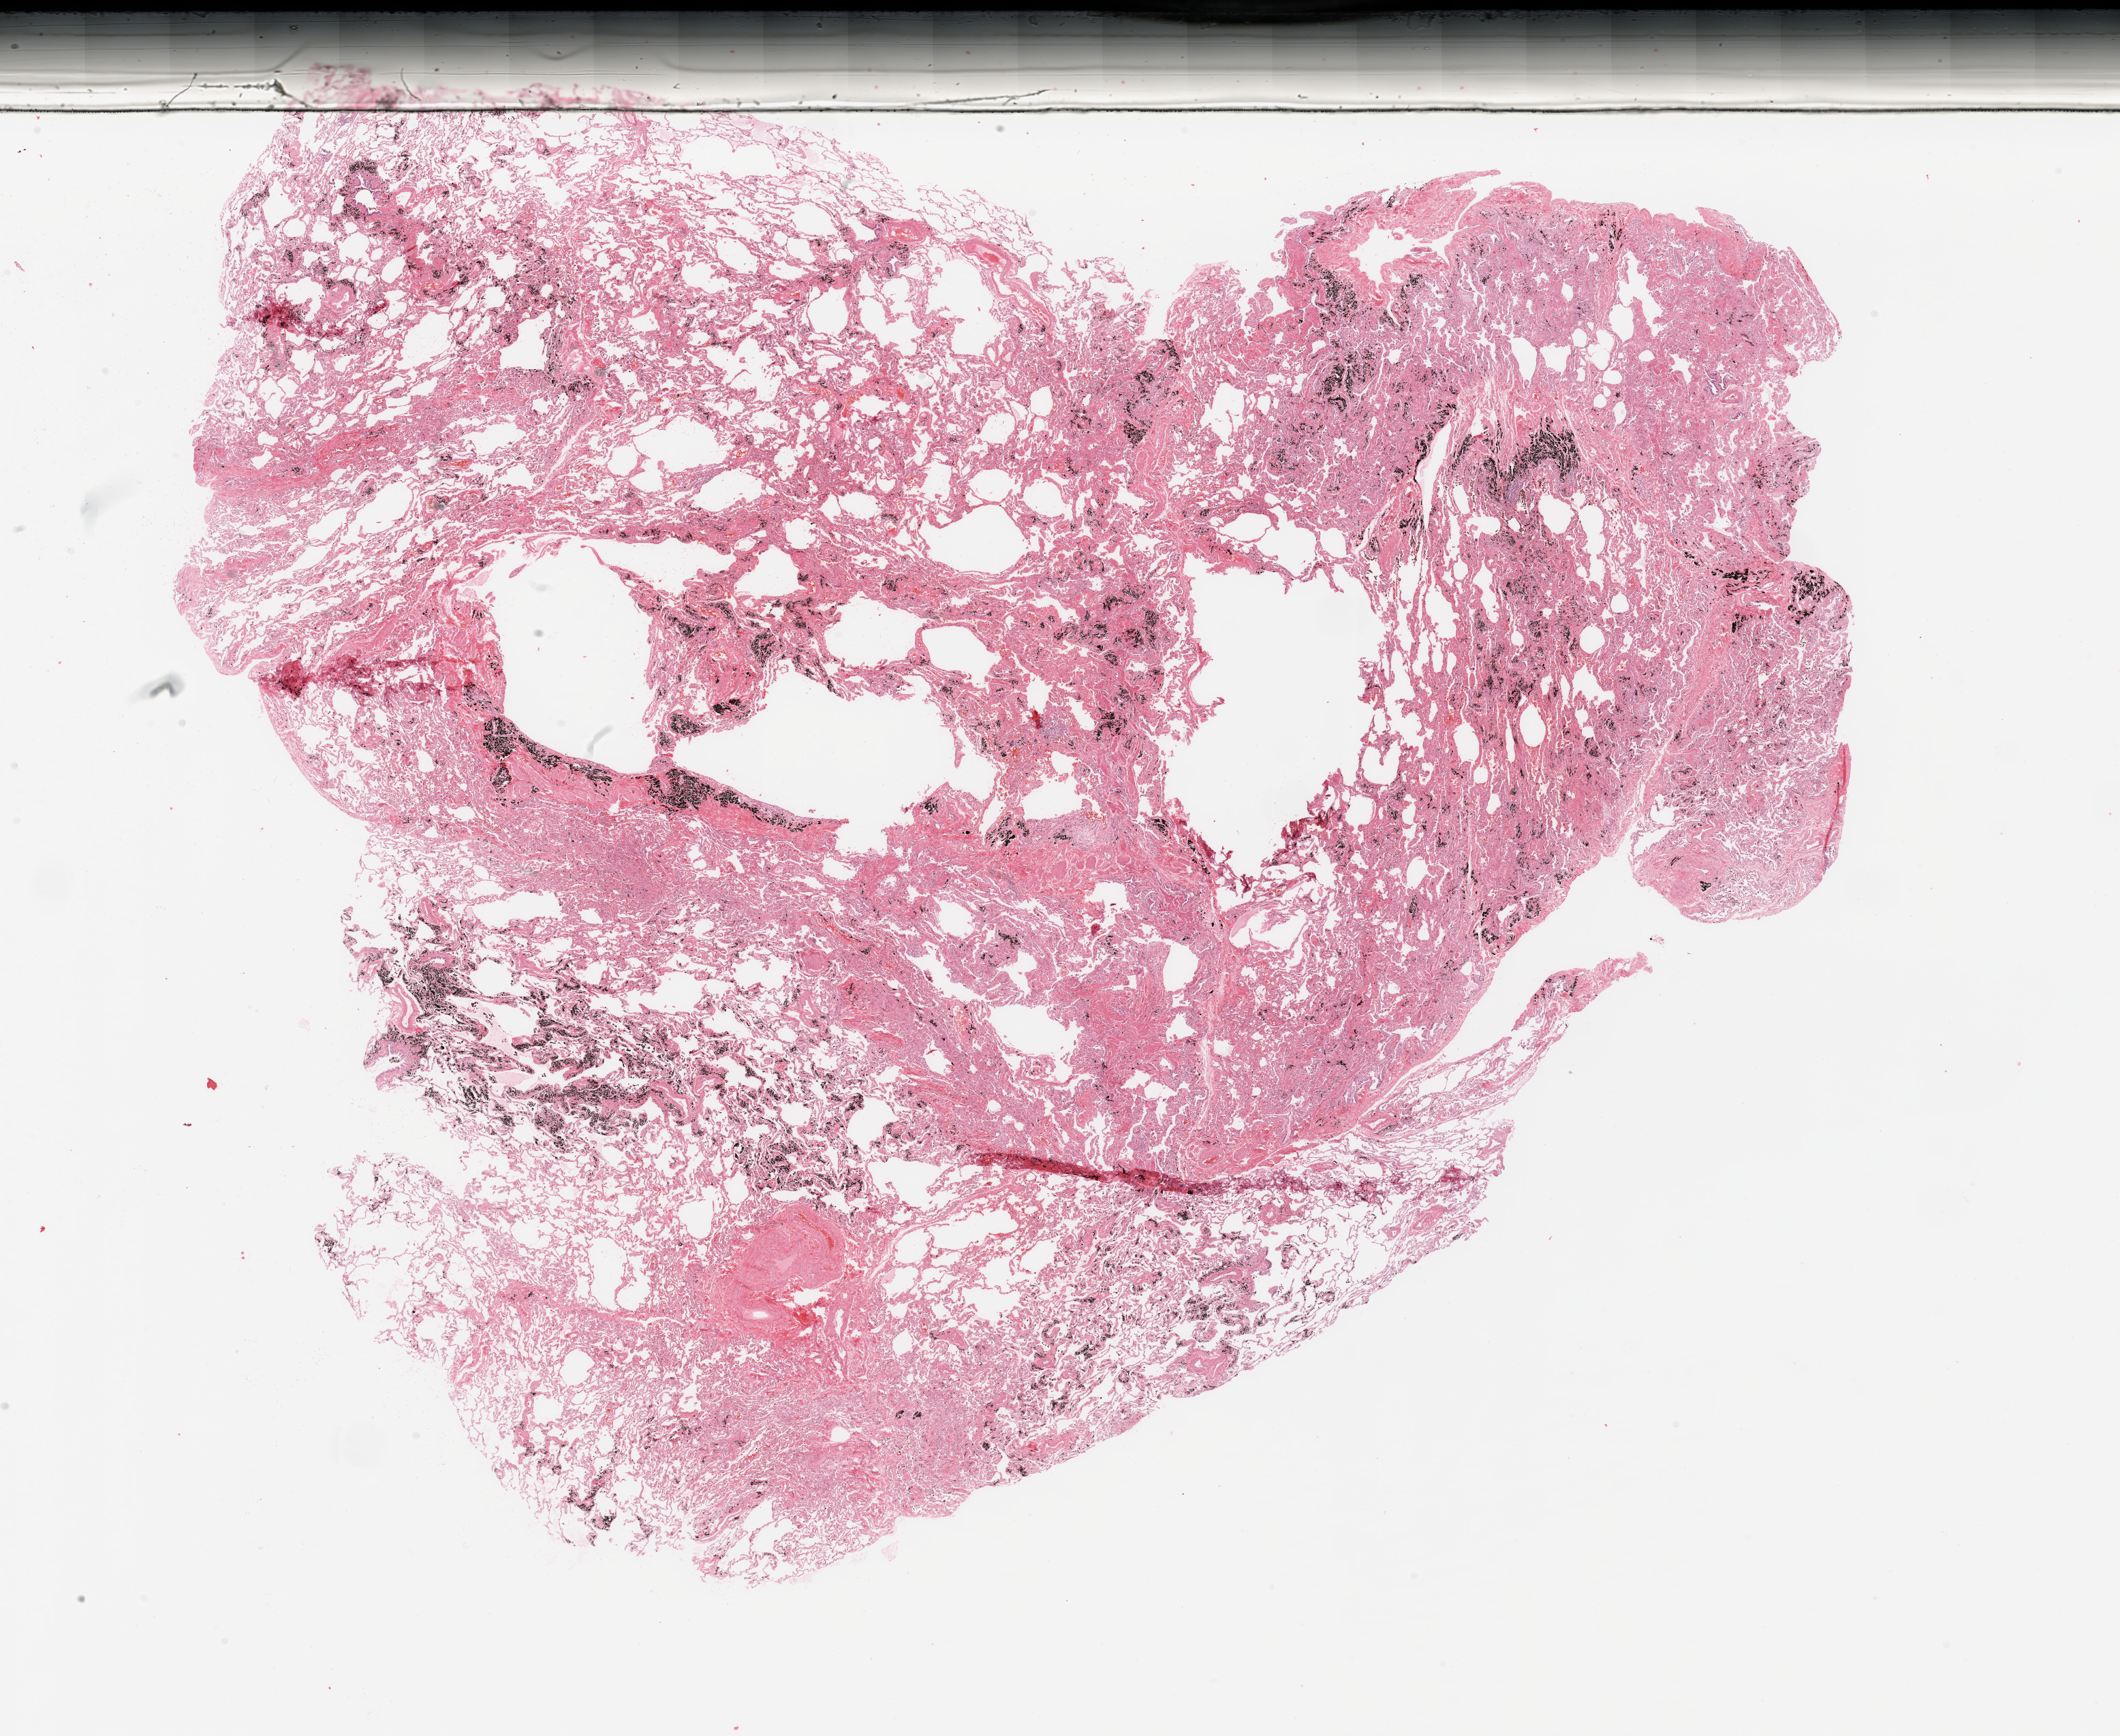
H&E-stained whole-slide image — shown as a low-resolution overview of the whole scanned area (about 24.6 x 20.2 mm); normal (non-tumour) tissue sample, lung. Patient: male, age 55 years.
* this section: normal (non-tumour) tissue from the same patient
* patient diagnosis: Adenocarcinoma, NOS